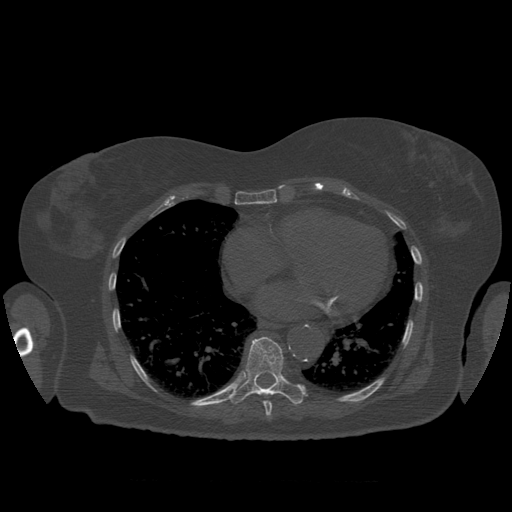
CT including the spine, one axial slice; reconstruction kernel STANDARD; 120 kVp; bone window (W 1800 / L 400 HU); 1.25 mm slice thickness; 512 × 512 image matrix. Patient age 81 years. Case-level facts recorded for this patient, not image findings: primary cancer: renal; vertebrae with lytic lesions (as recorded): L1.
Annotated regions visible in this slice (semi-automatically segmented with operator editing):
- T8 vertebra: bounding box <263,401,272,418> (left, top, right, bottom; pixels)
- T9 vertebra: <229,337,305,405>